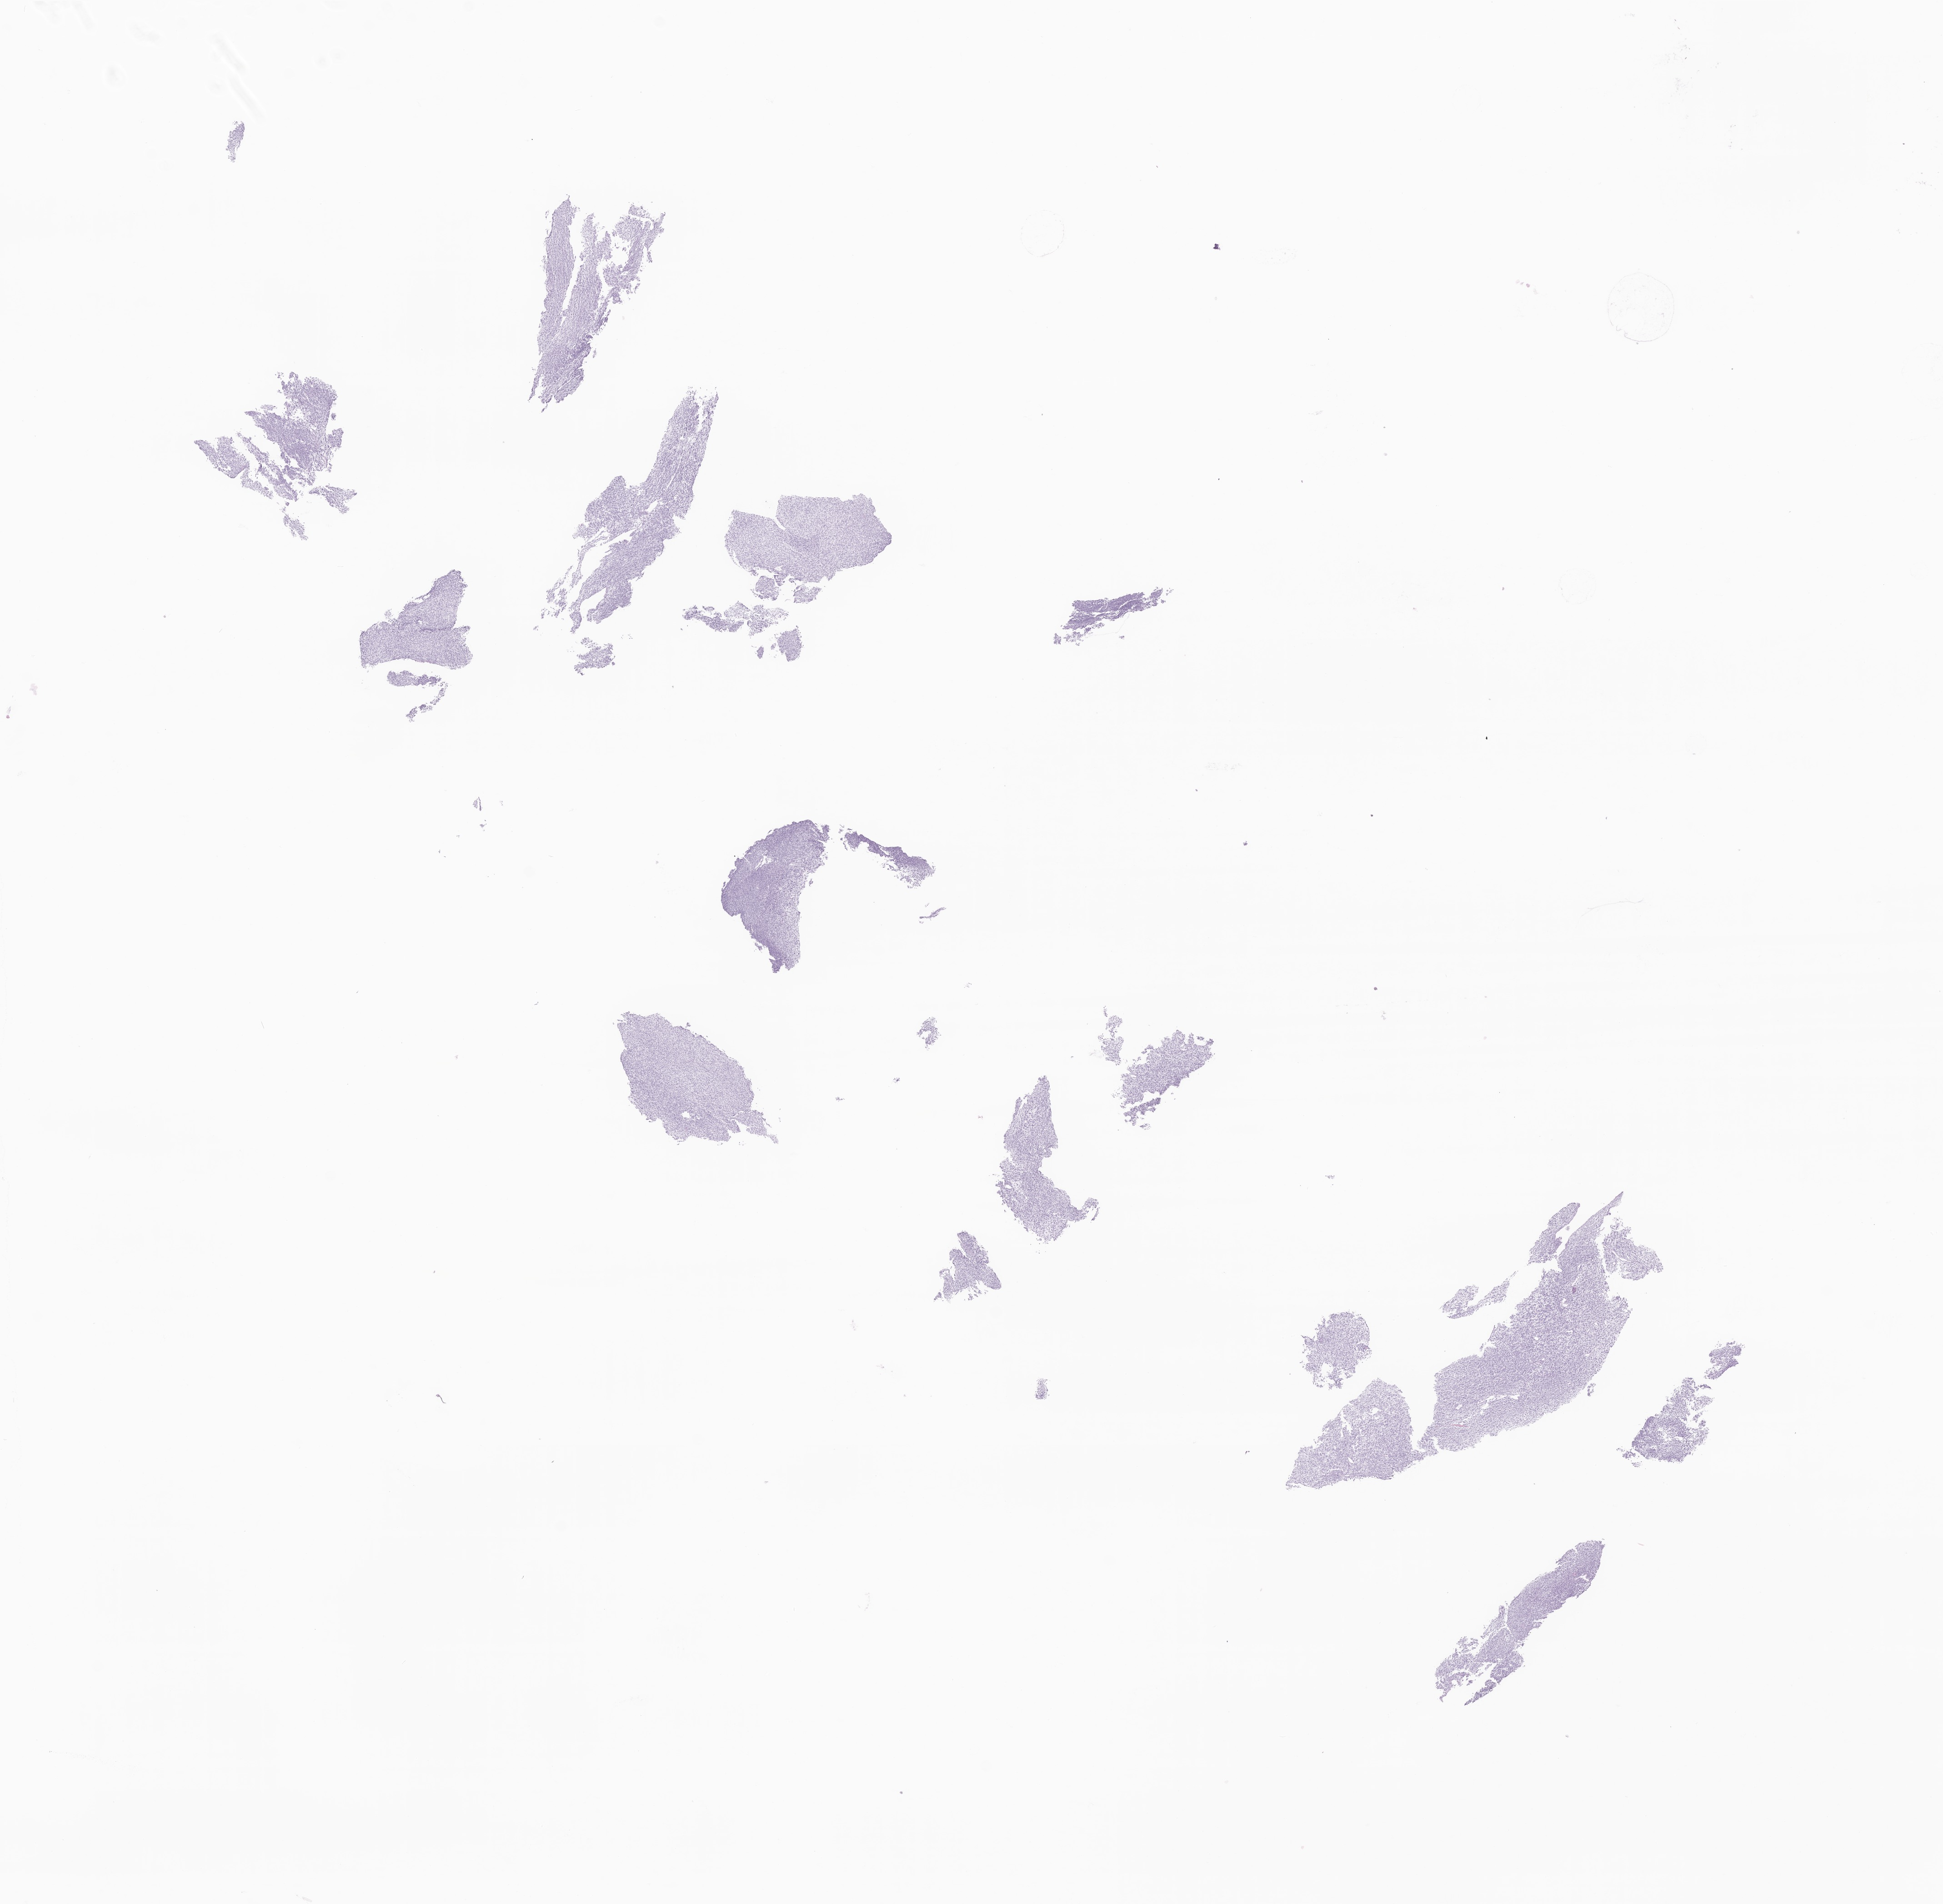
H&E whole-slide image of tumor tissue from the prostate, a low-resolution overview of the entire scanned area, about 18.0 x 17.7 mm, formalin-fixed paraffin-embedded section. Patient male; age 134 months (11 years 2 months).
* diagnosis (ICD-O-3 morphology term): Rhabdomyosarcoma, NOS